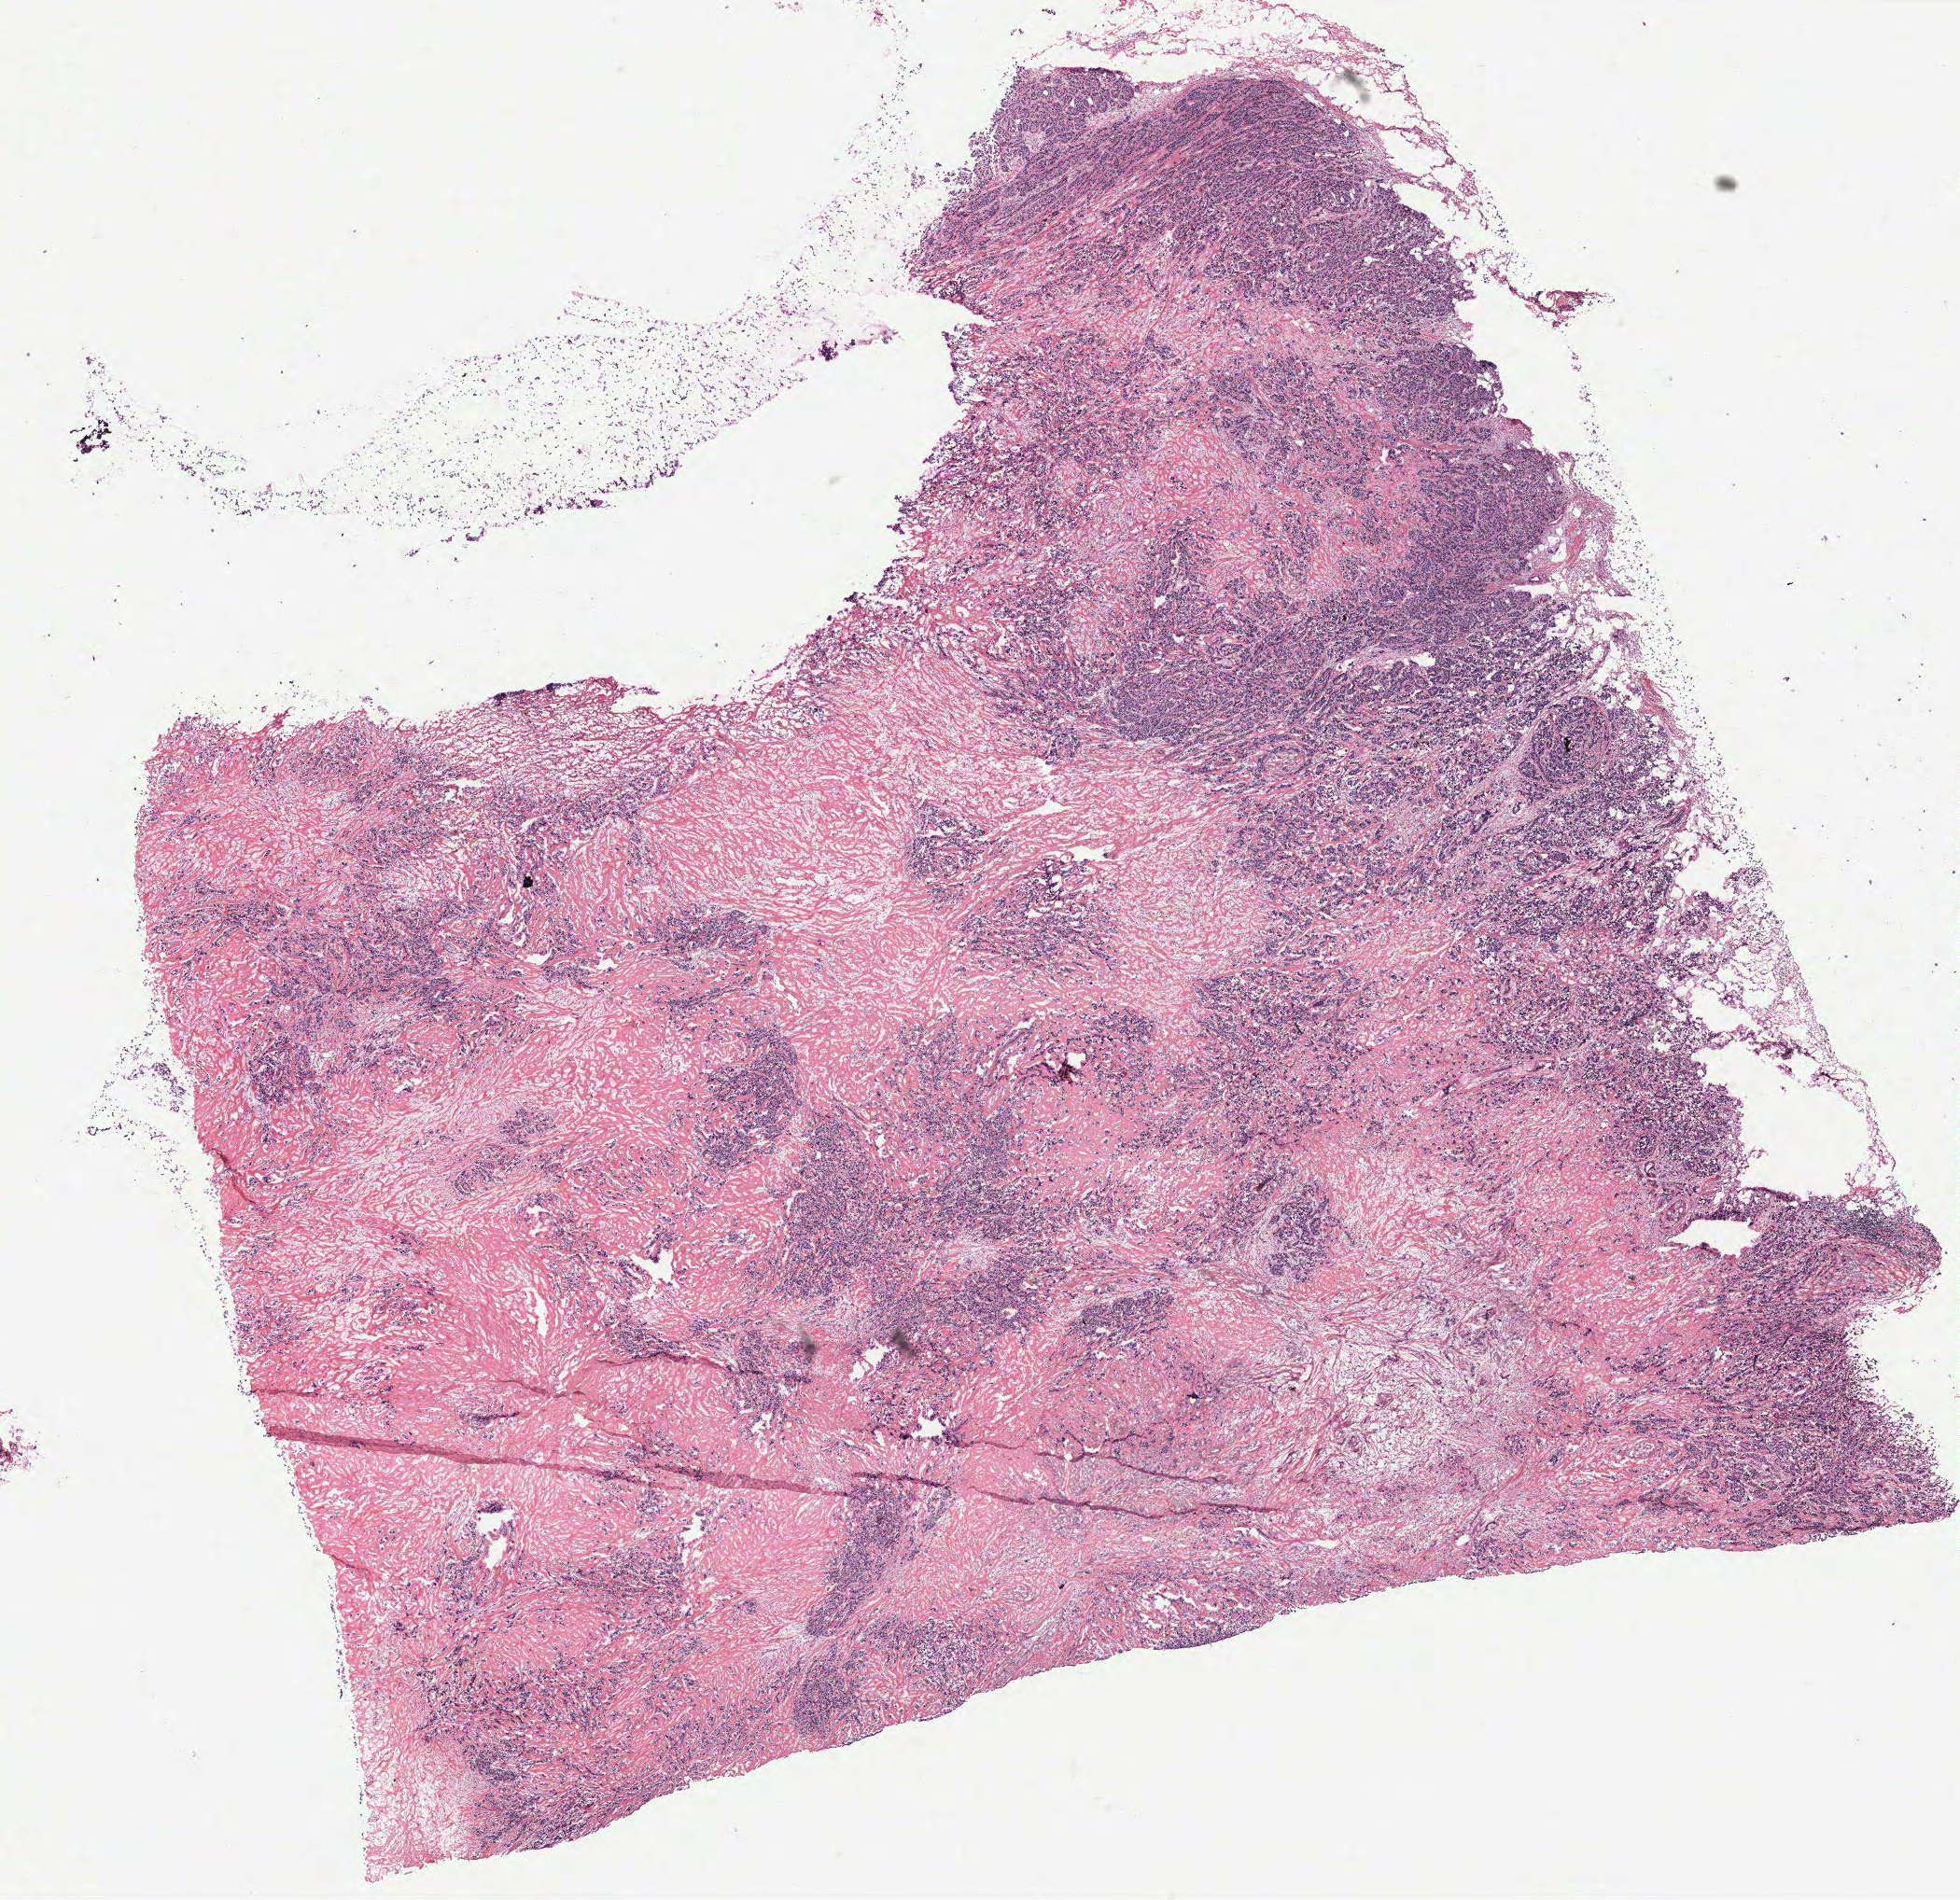
Hematoxylin and eosin (H&E) stained whole-slide image — low-resolution overview of the scanned area, about 16.8 x 16.3 mm (acquisition: 40x scan). Breast, tumour tissue. Female, 61 y/o.
Histologic diagnosis: Infiltrating duct carcinoma, NOS. AJCC pathologic stage: IIA.